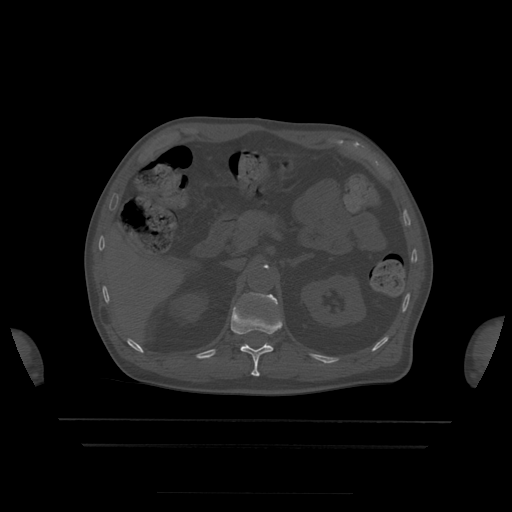
CT including the spine, one axial slice; bone window (W 1800 / L 400 HU); 1.25 mm slice thickness; 512 × 512 image matrix, field of view 436 × 436 mm. Patient age 68 years. Case-level facts recorded for this patient, not image findings: primary cancer: urothelial.
Annotated regions visible in this slice (semi-automatically segmented with operator editing):
- L1 vertebra: bounding box (x1, y1, x2, y2) in pixels: (248, 293, 278, 306)
- T12 vertebra: (231, 307, 283, 377)